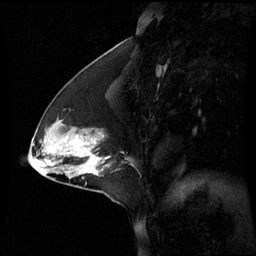
Breast MRI (dynamic contrast-enhanced), one sagittal slice. Position 27 of 60 along the scan axis. Dynamic contrast-enhanced series, image 2 of 3 at this slice position (ordered by acquisition). 1.5 T. TE 4.2 ms, TR 8.9 ms. 256 × 256 image matrix. Patient: female, 44 years. From the clinical record (not read from this slice): setting: breast cancer imaged before/during neoadjuvant chemotherapy; receptor status: triple-negative.
Annotated regions visible in this slice (semi-automatically segmented with operator editing):
- analysis volume of interest (the breast-tissue region the enhancement analysis was run in; not a lesion): bounding box <76,150,102,177> (left, top, right, bottom; pixels)
- tumour enhancement mask (voxels above the 70 % enhancement threshold inside the analysis volume of interest): <91,170,96,175>